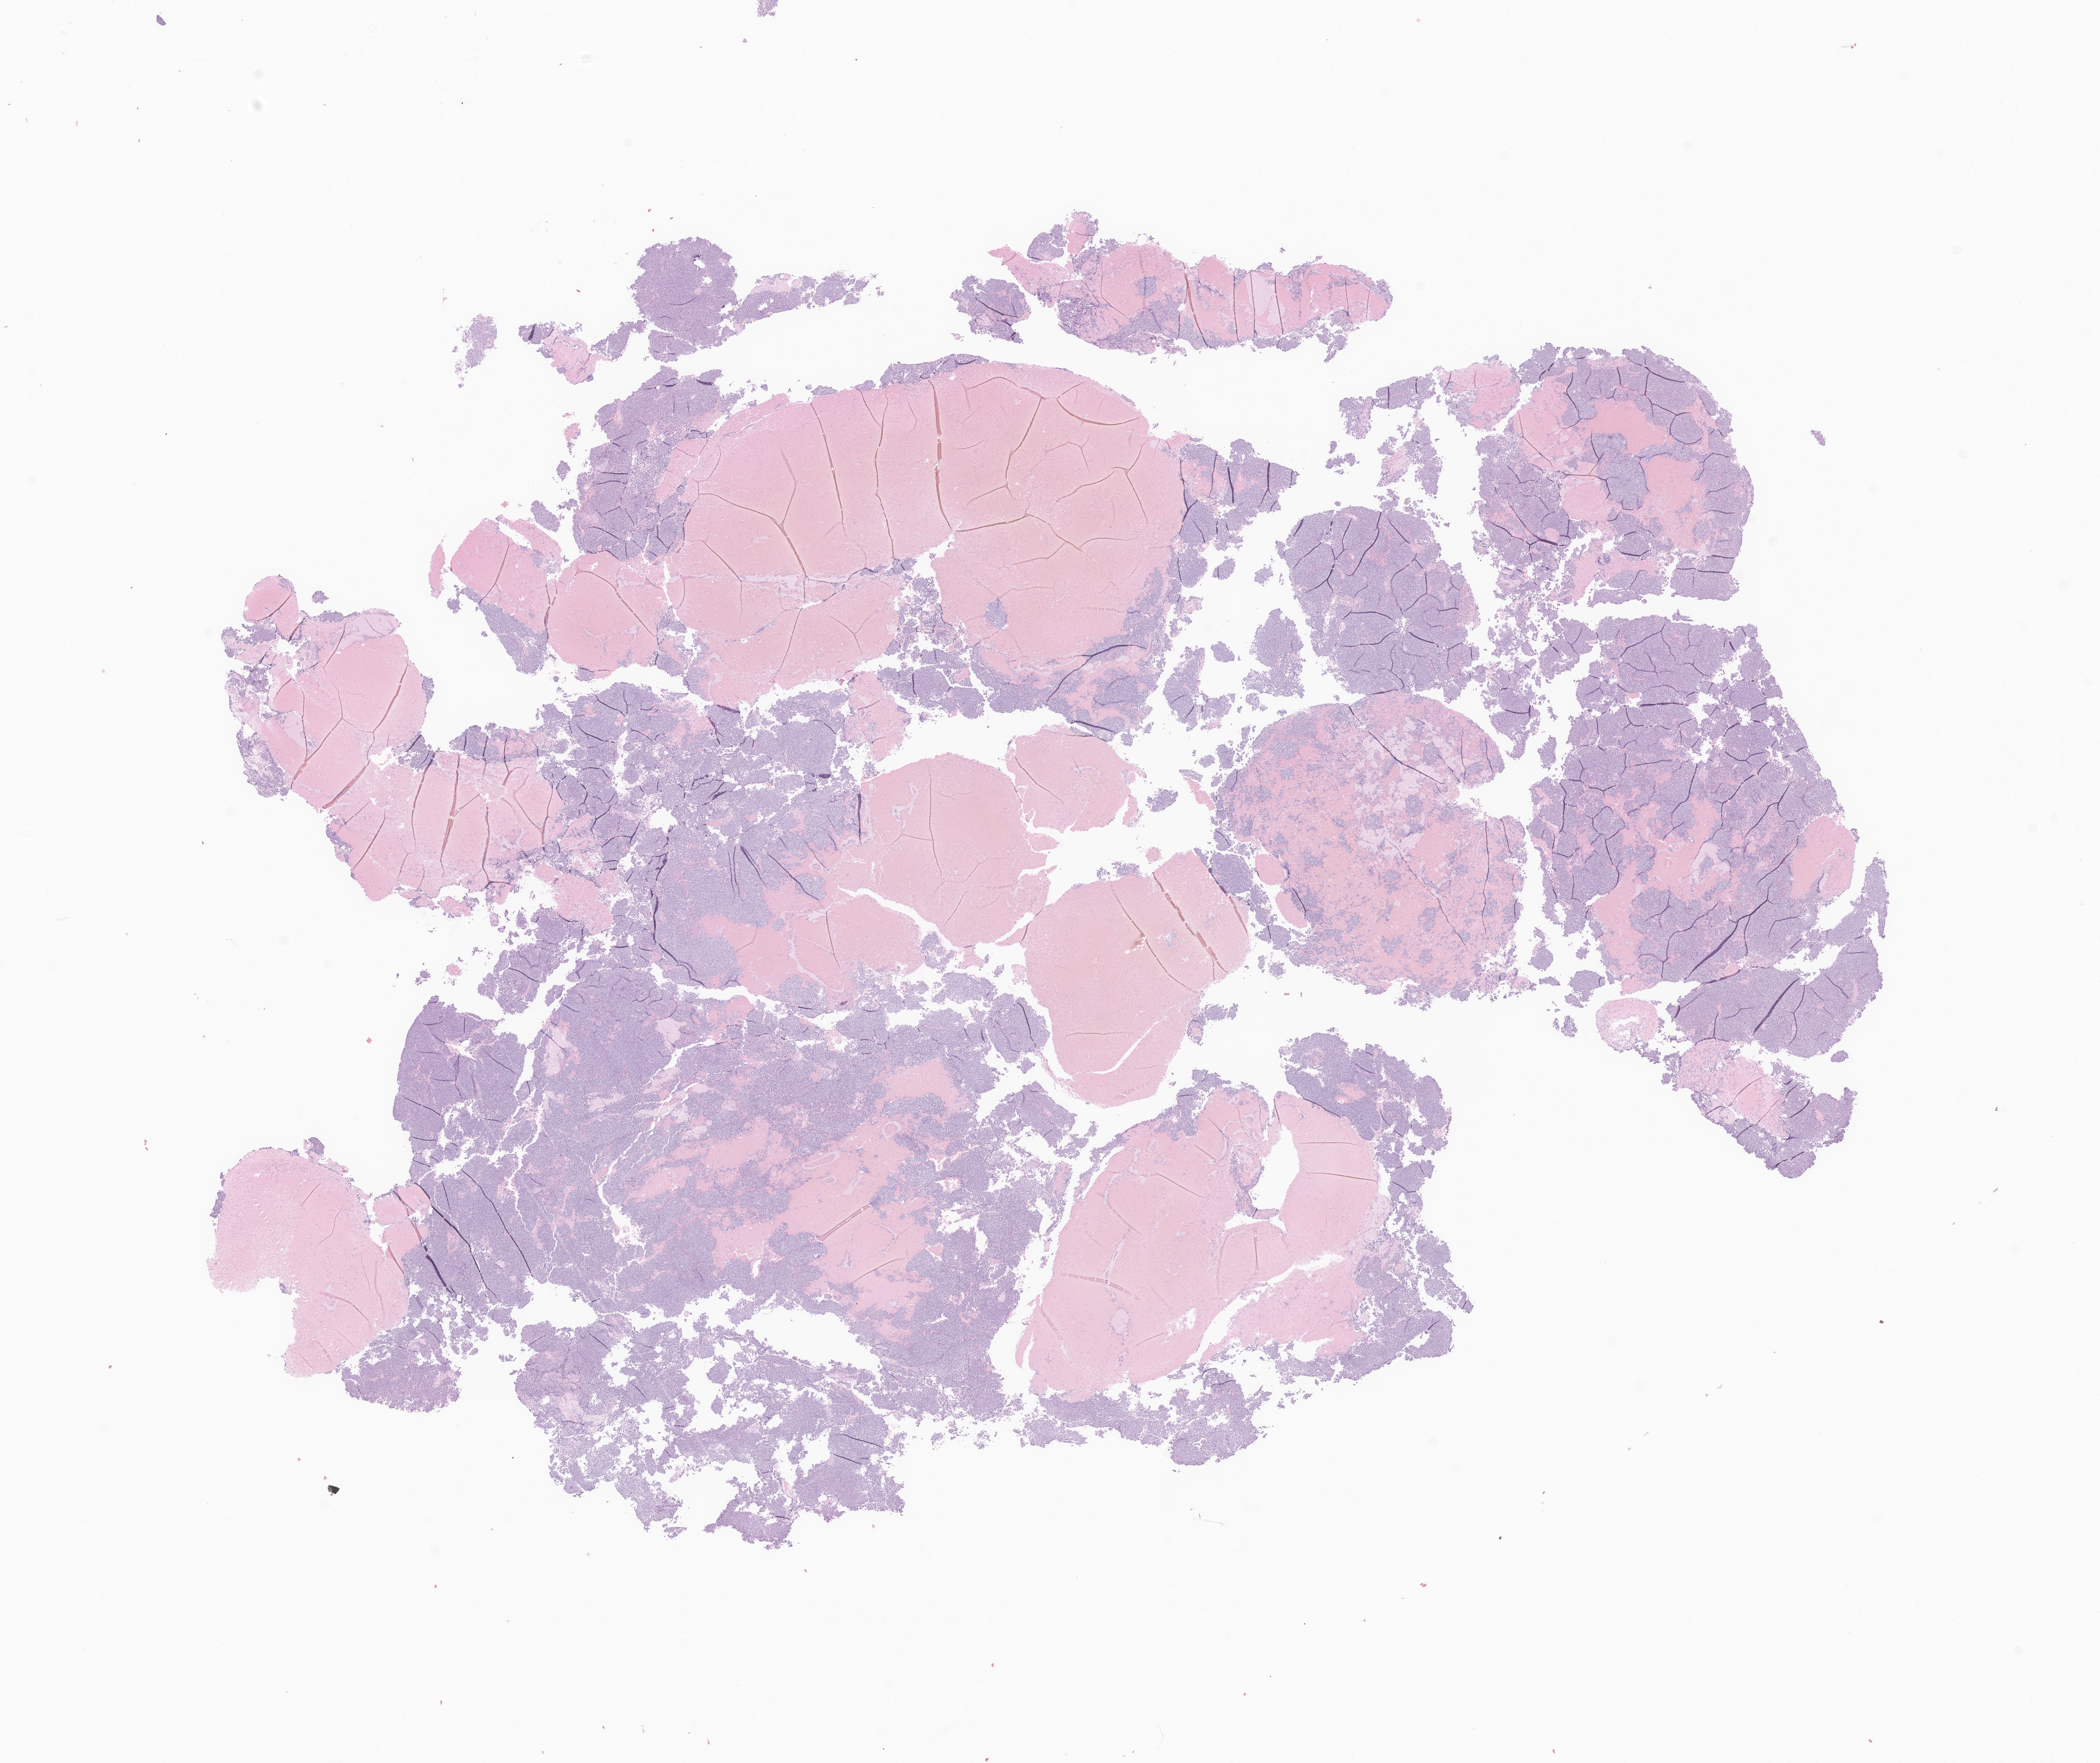
Hematoxylin and eosin (H&E) whole-slide image of tumor tissue from the brain, low-resolution overview of the scanned area, about 18.5 x 15.5 mm; formalin-fixed paraffin-embedded section. Patient: female, age 154 months (12 years 10 months).
Recorded diagnosis: Medulloblastoma, NOS.